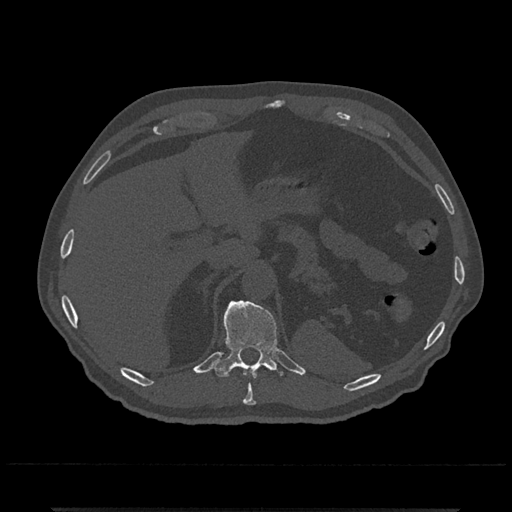
CT including the spine, one axial slice; position 507 of 797 along the scan axis; reconstruction kernel Br40s/3; 120 kVp; bone window (W 1800 / L 400 HU); 0.5 mm slice thickness; 512 × 512 image matrix, field of view 393 × 393 mm. Male patient, age 67 years. Case-level facts recorded for this patient, not image findings: primary cancer: prostate.
Structures marked on this image (semi-automatically segmented with operator editing):
- T10 vertebra: box from (x=243, y=374) to (x=256, y=405) px
- T11 vertebra: (x=213, y=300)–(x=284, y=378)